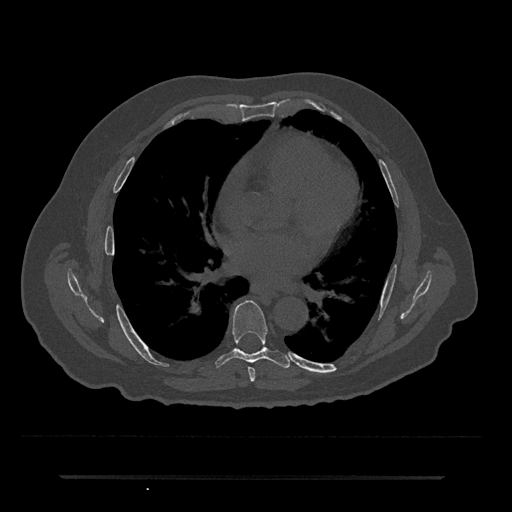
CT including the spine, one axial slice. 120 kVp. Bone window (W 1800 / L 400 HU). 0.5 mm slice thickness. 512 × 512 image matrix, field of view 437 × 437 mm. Patient: male, 69 years. From the clinical record (not read from this slice): primary cancer: prostate.
Annotated regions visible in this slice (semi-automatically segmented with operator editing):
- T6 vertebra: bounding box <248,367,255,381> (left, top, right, bottom; pixels)
- T7 vertebra: <216,300,290,368>